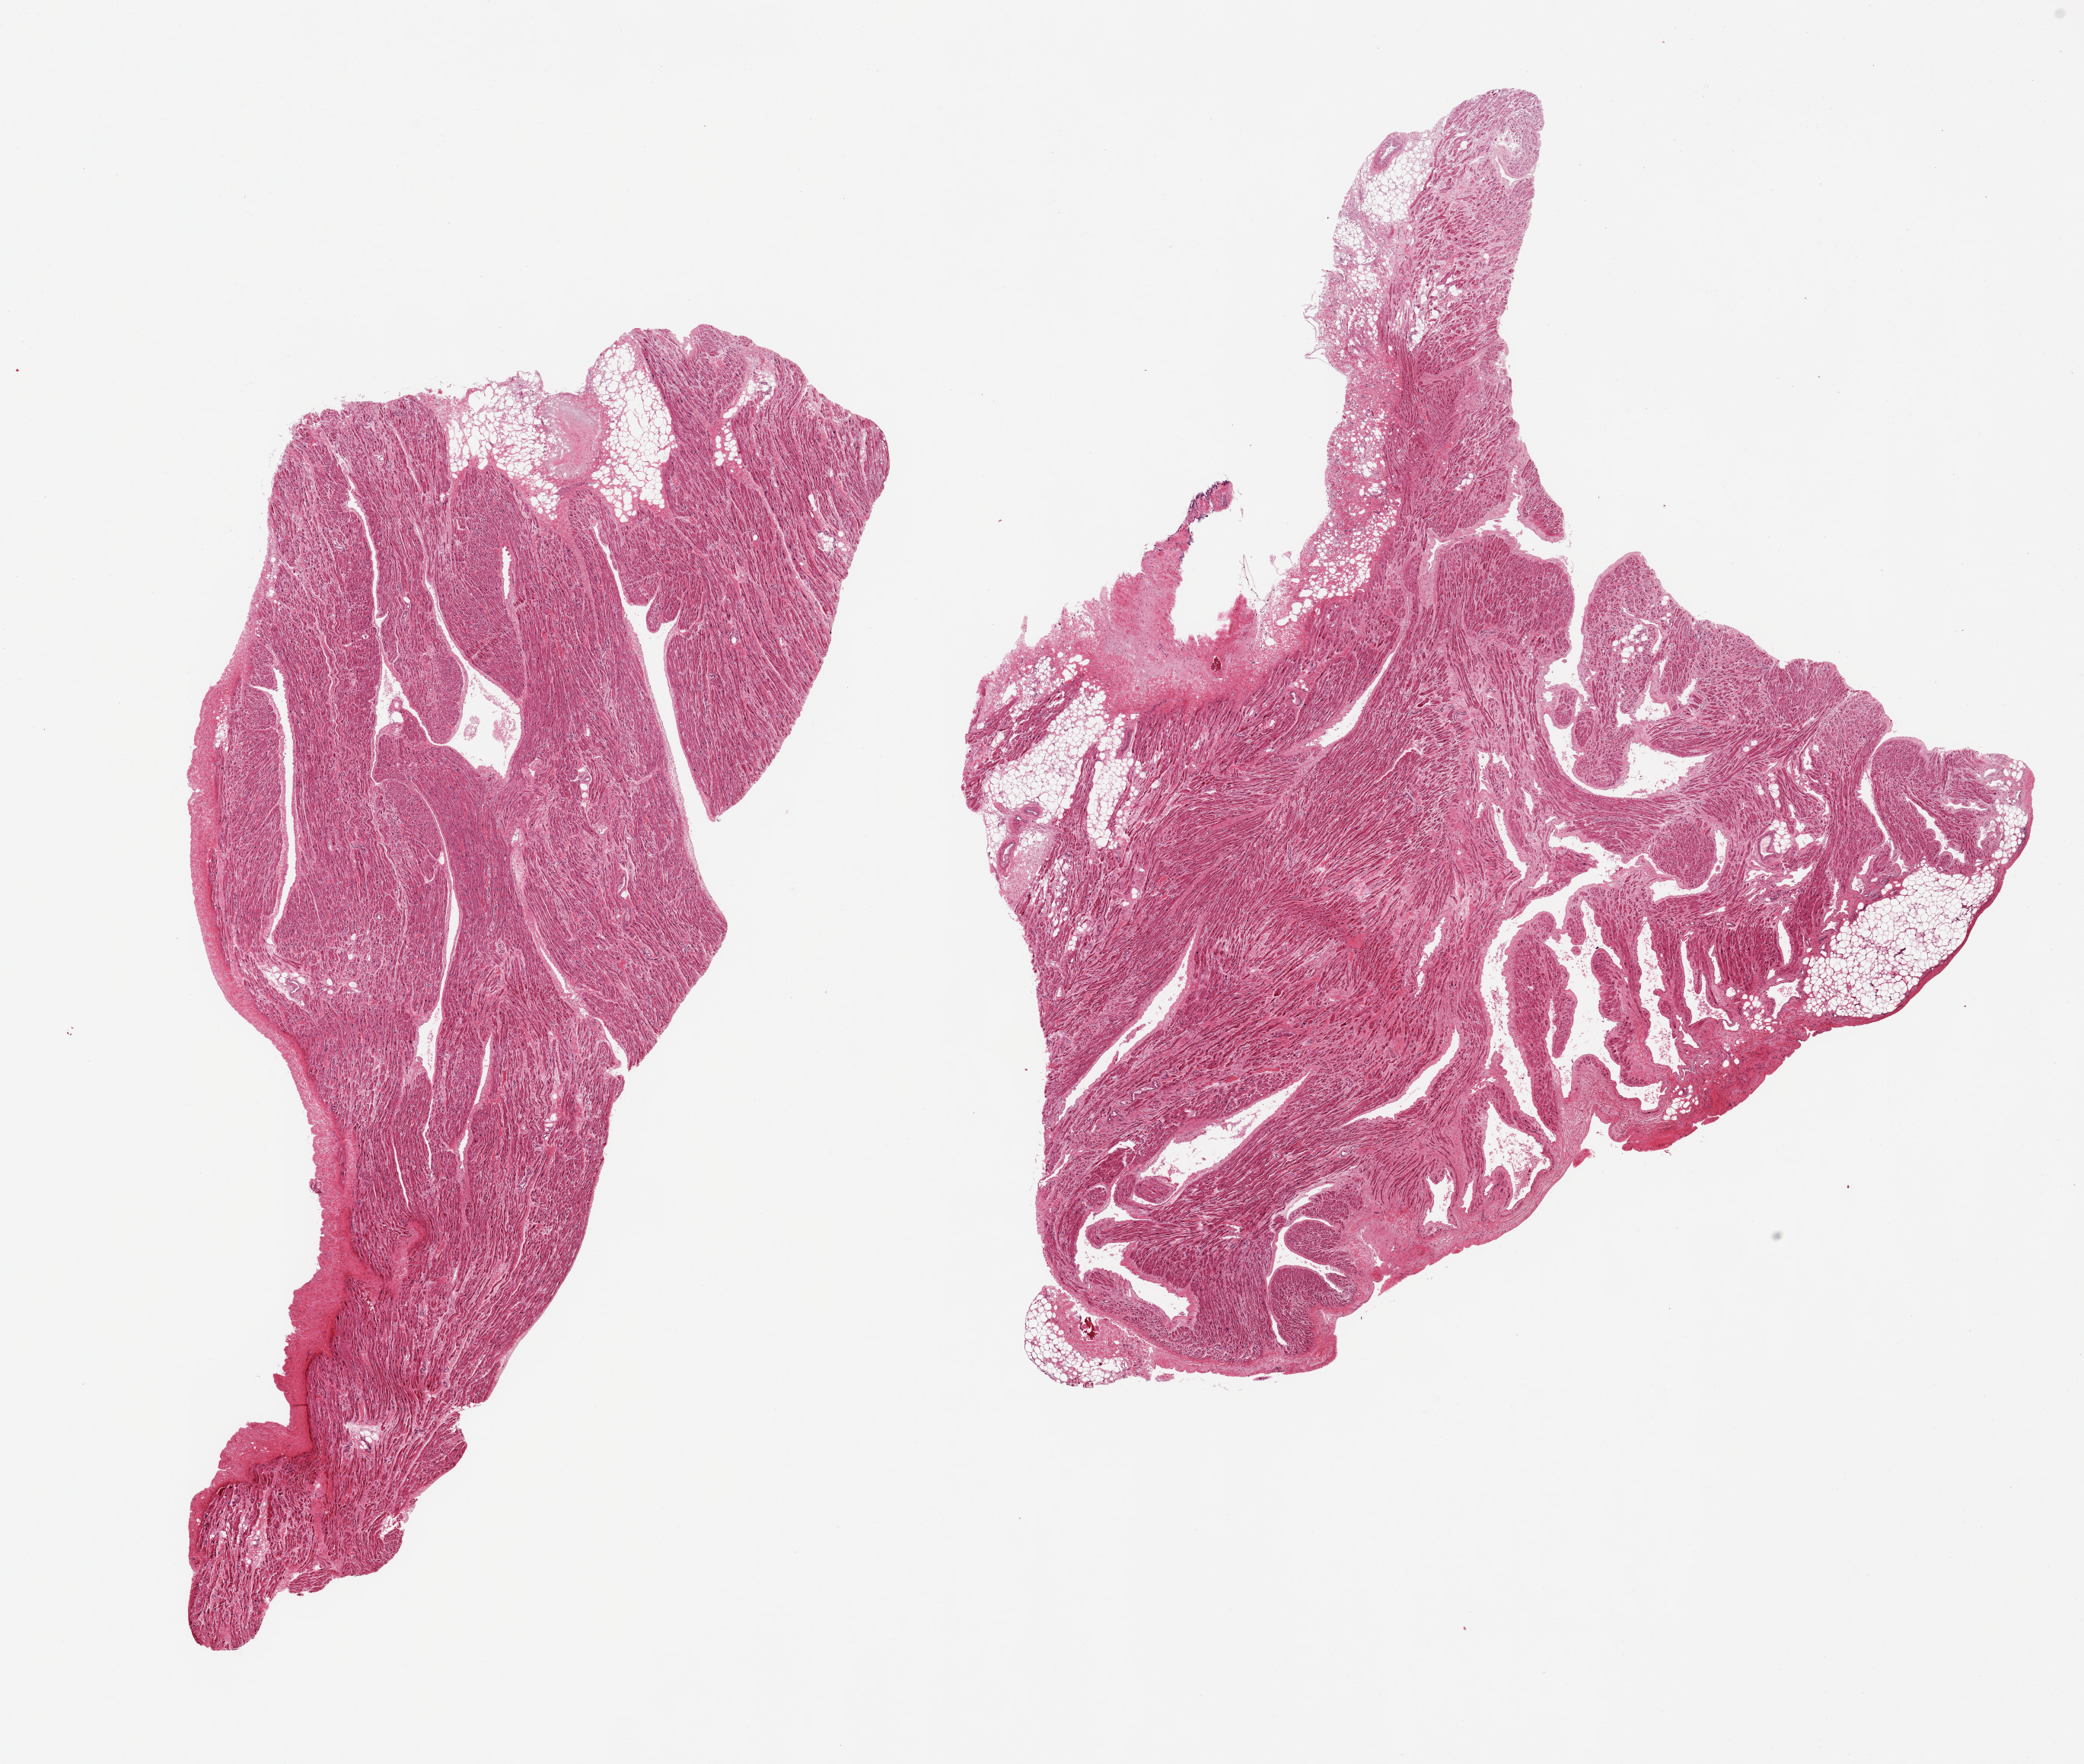
Hematoxylin and eosin (H&E) whole-slide image, a low-resolution overview of the entire scanned area, about 21.7 x 18.3 mm (acquisition: 20x scan), PAXgene-fixed, paraffin-embedded tissue, target tissue: auricular appendage, tissue donor sample. Female donor.
Review note (as recorded): 2 pieces; 5 & 10% internal fat content.